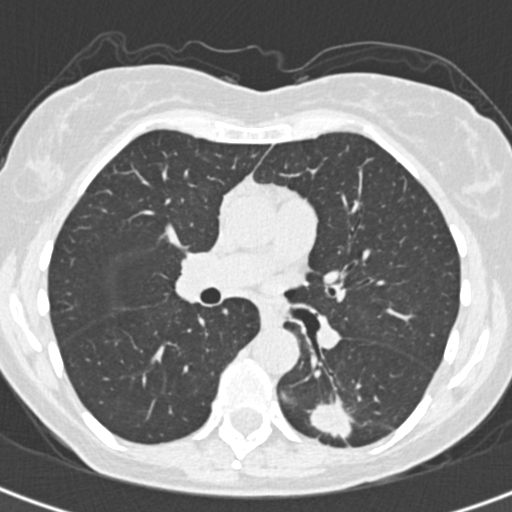
Low-dose screening chest CT, one axial slice. Slice 193 of 328 in the series (ordered by position). Reconstruction kernel B30f. 120 kVp. Lung window (W 1500 / L -600 HU). 1 mm slice thickness. 512 × 512 image matrix, field of view 284 × 284 mm.
Structures marked on this image (outlined manually by an expert reader):
- lesion 1 (tumor, lower lobe of left lung): bounding box [x1, y1, x2, y2] px = [310, 398, 353, 439]